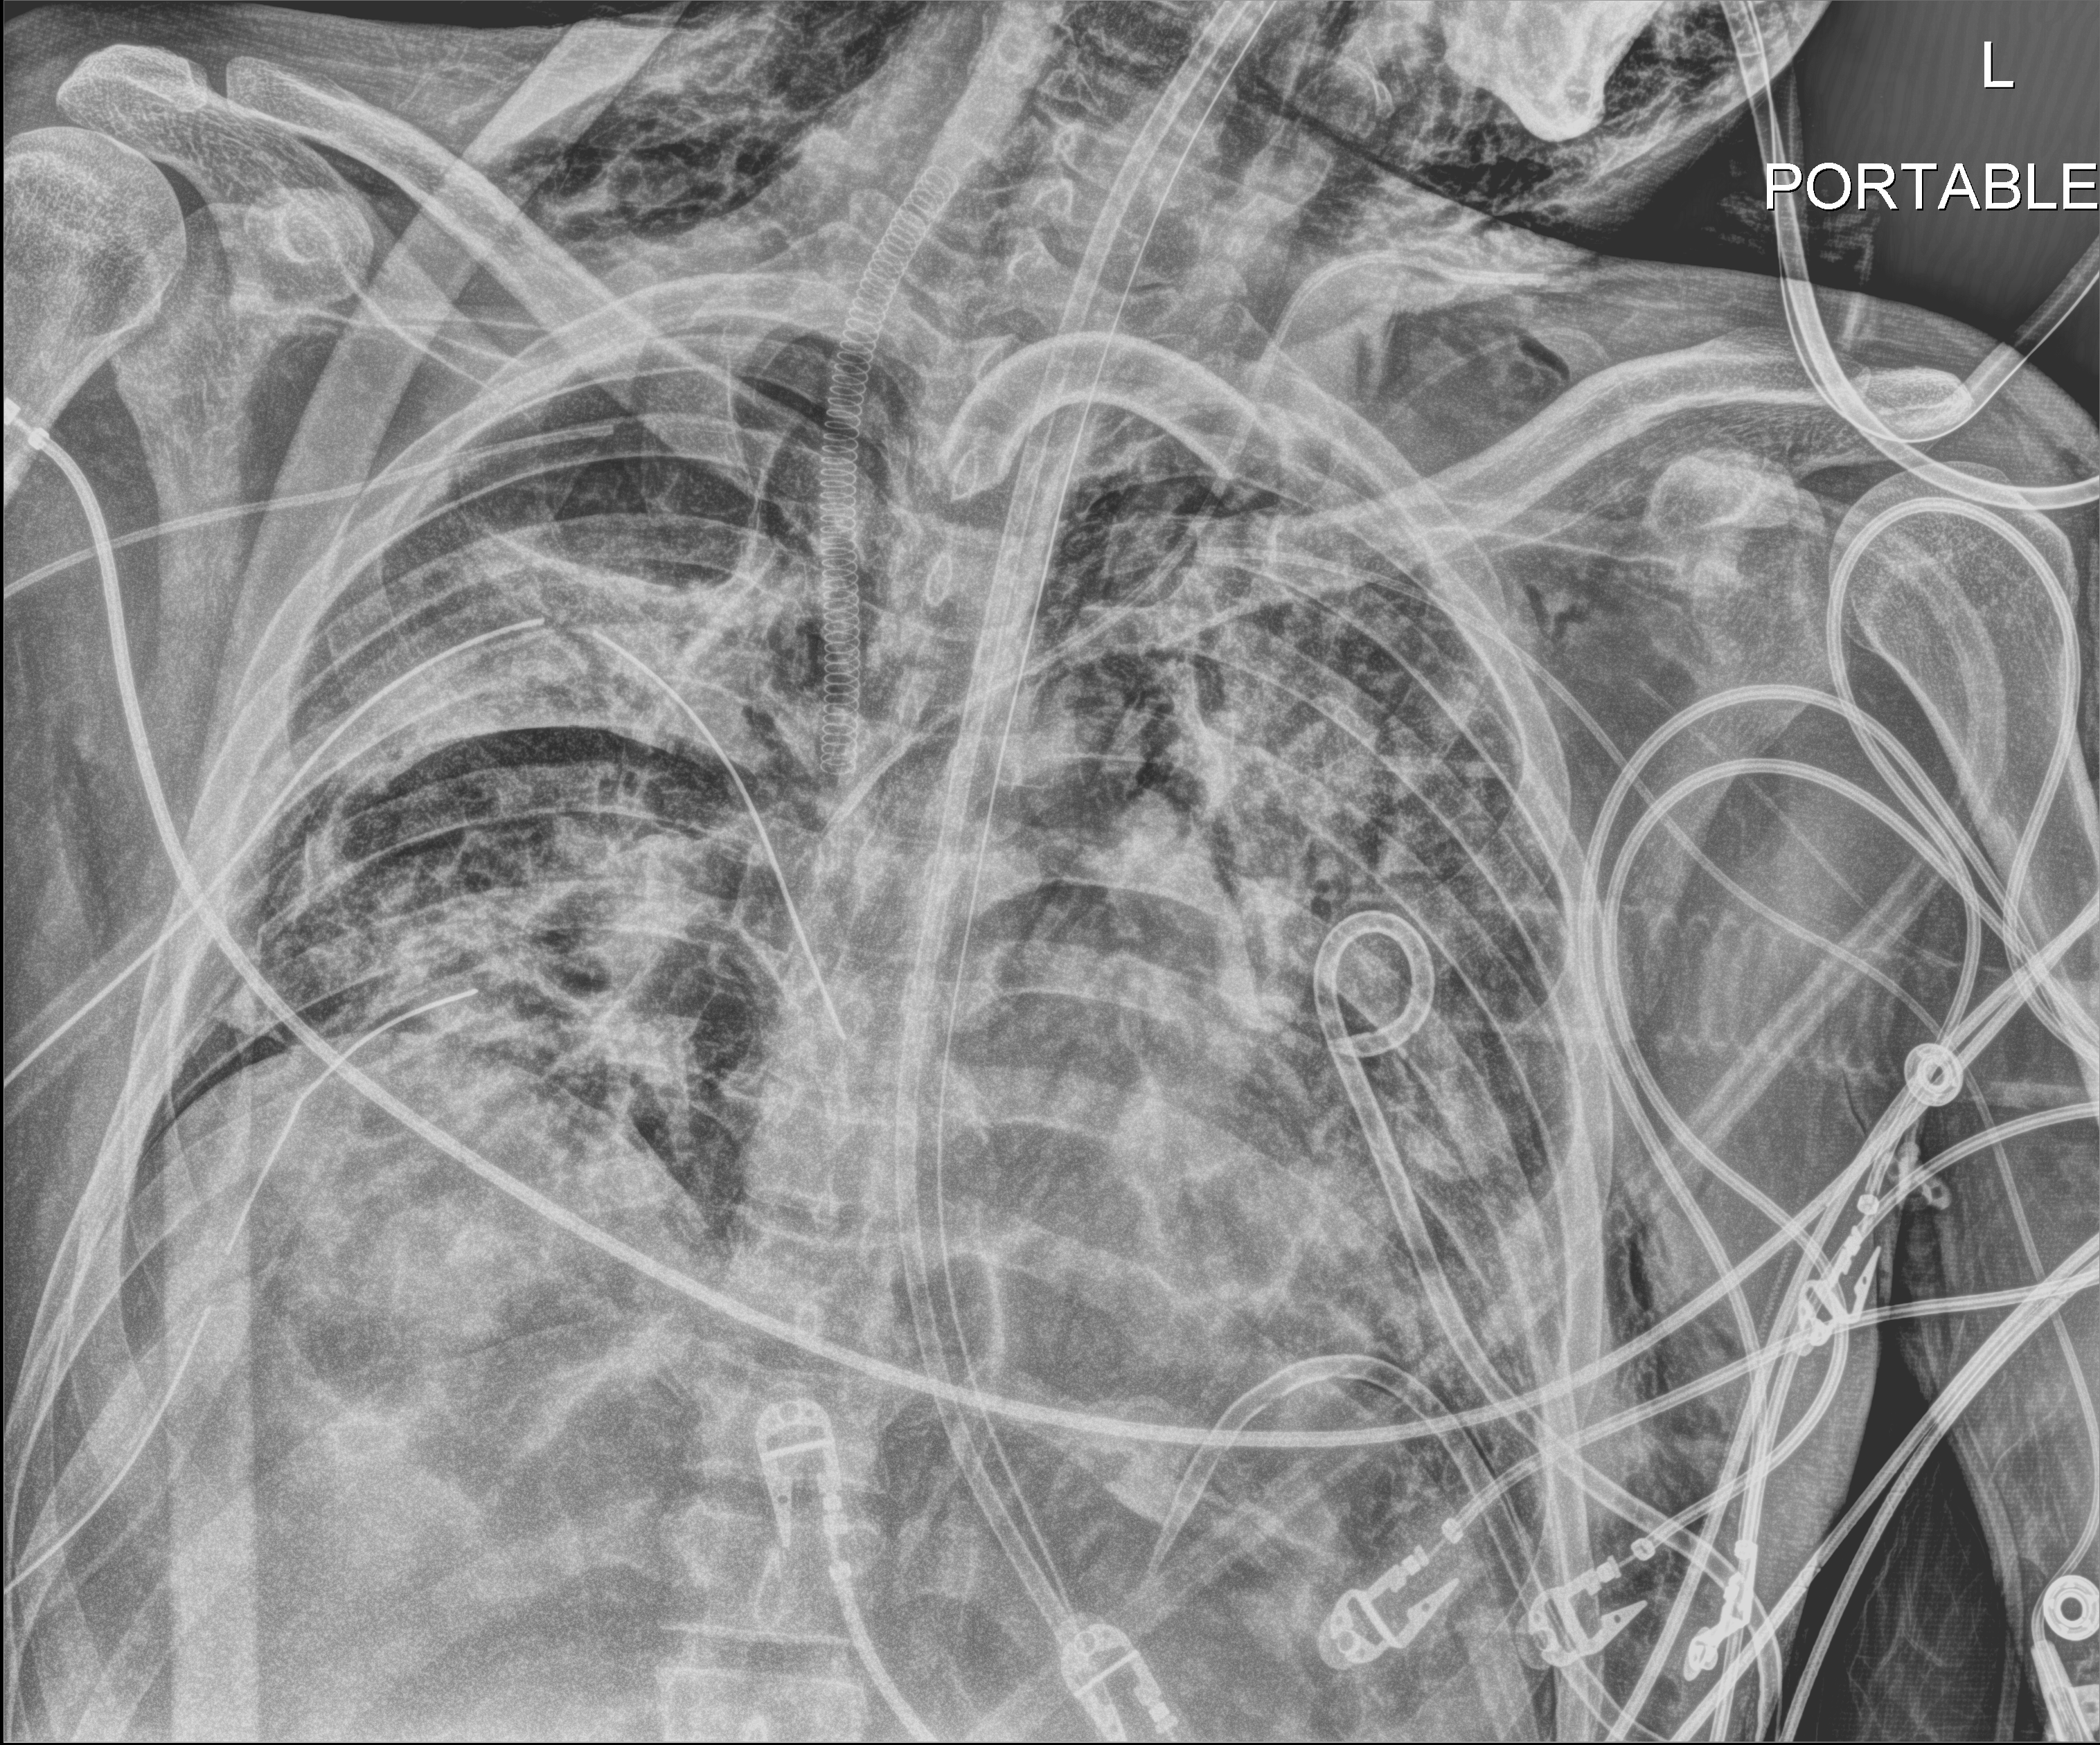
Portable chest radiograph; anteroposterior (AP) projection. Adult patient hospitalised with COVID-19, age 18–59 years.
Hospital-stay facts (about this admission, not read from this image; timing relative to this image not recorded):
- COPD (admission record): no
- diabetes (admission record): no